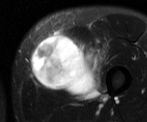
MRI of an extremity soft-tissue mass, one axial slice. Slice 19 of 52 in the series (ordered by position). T2-weighted fat-saturated. MR volume resampled by the dataset authors to the PET/CT grid (not the native acquisition matrix). 147 × 122 image matrix, field of view 144 × 119 mm. Male patient. From the clinical record (not read from this slice): histological type: pleiomorphic liposarcoma; grade: high; site of the primary tumour: left thigh.
Annotated regions visible in this slice (expert contour drawn on MRI and transferred to this co-registered scan by the dataset authors):
- gross tumour volume including surrounding oedema: bounding box [x1, y1, x2, y2] px = [30, 28, 106, 102]
- gross tumour volume (mass): [30, 32, 97, 95]